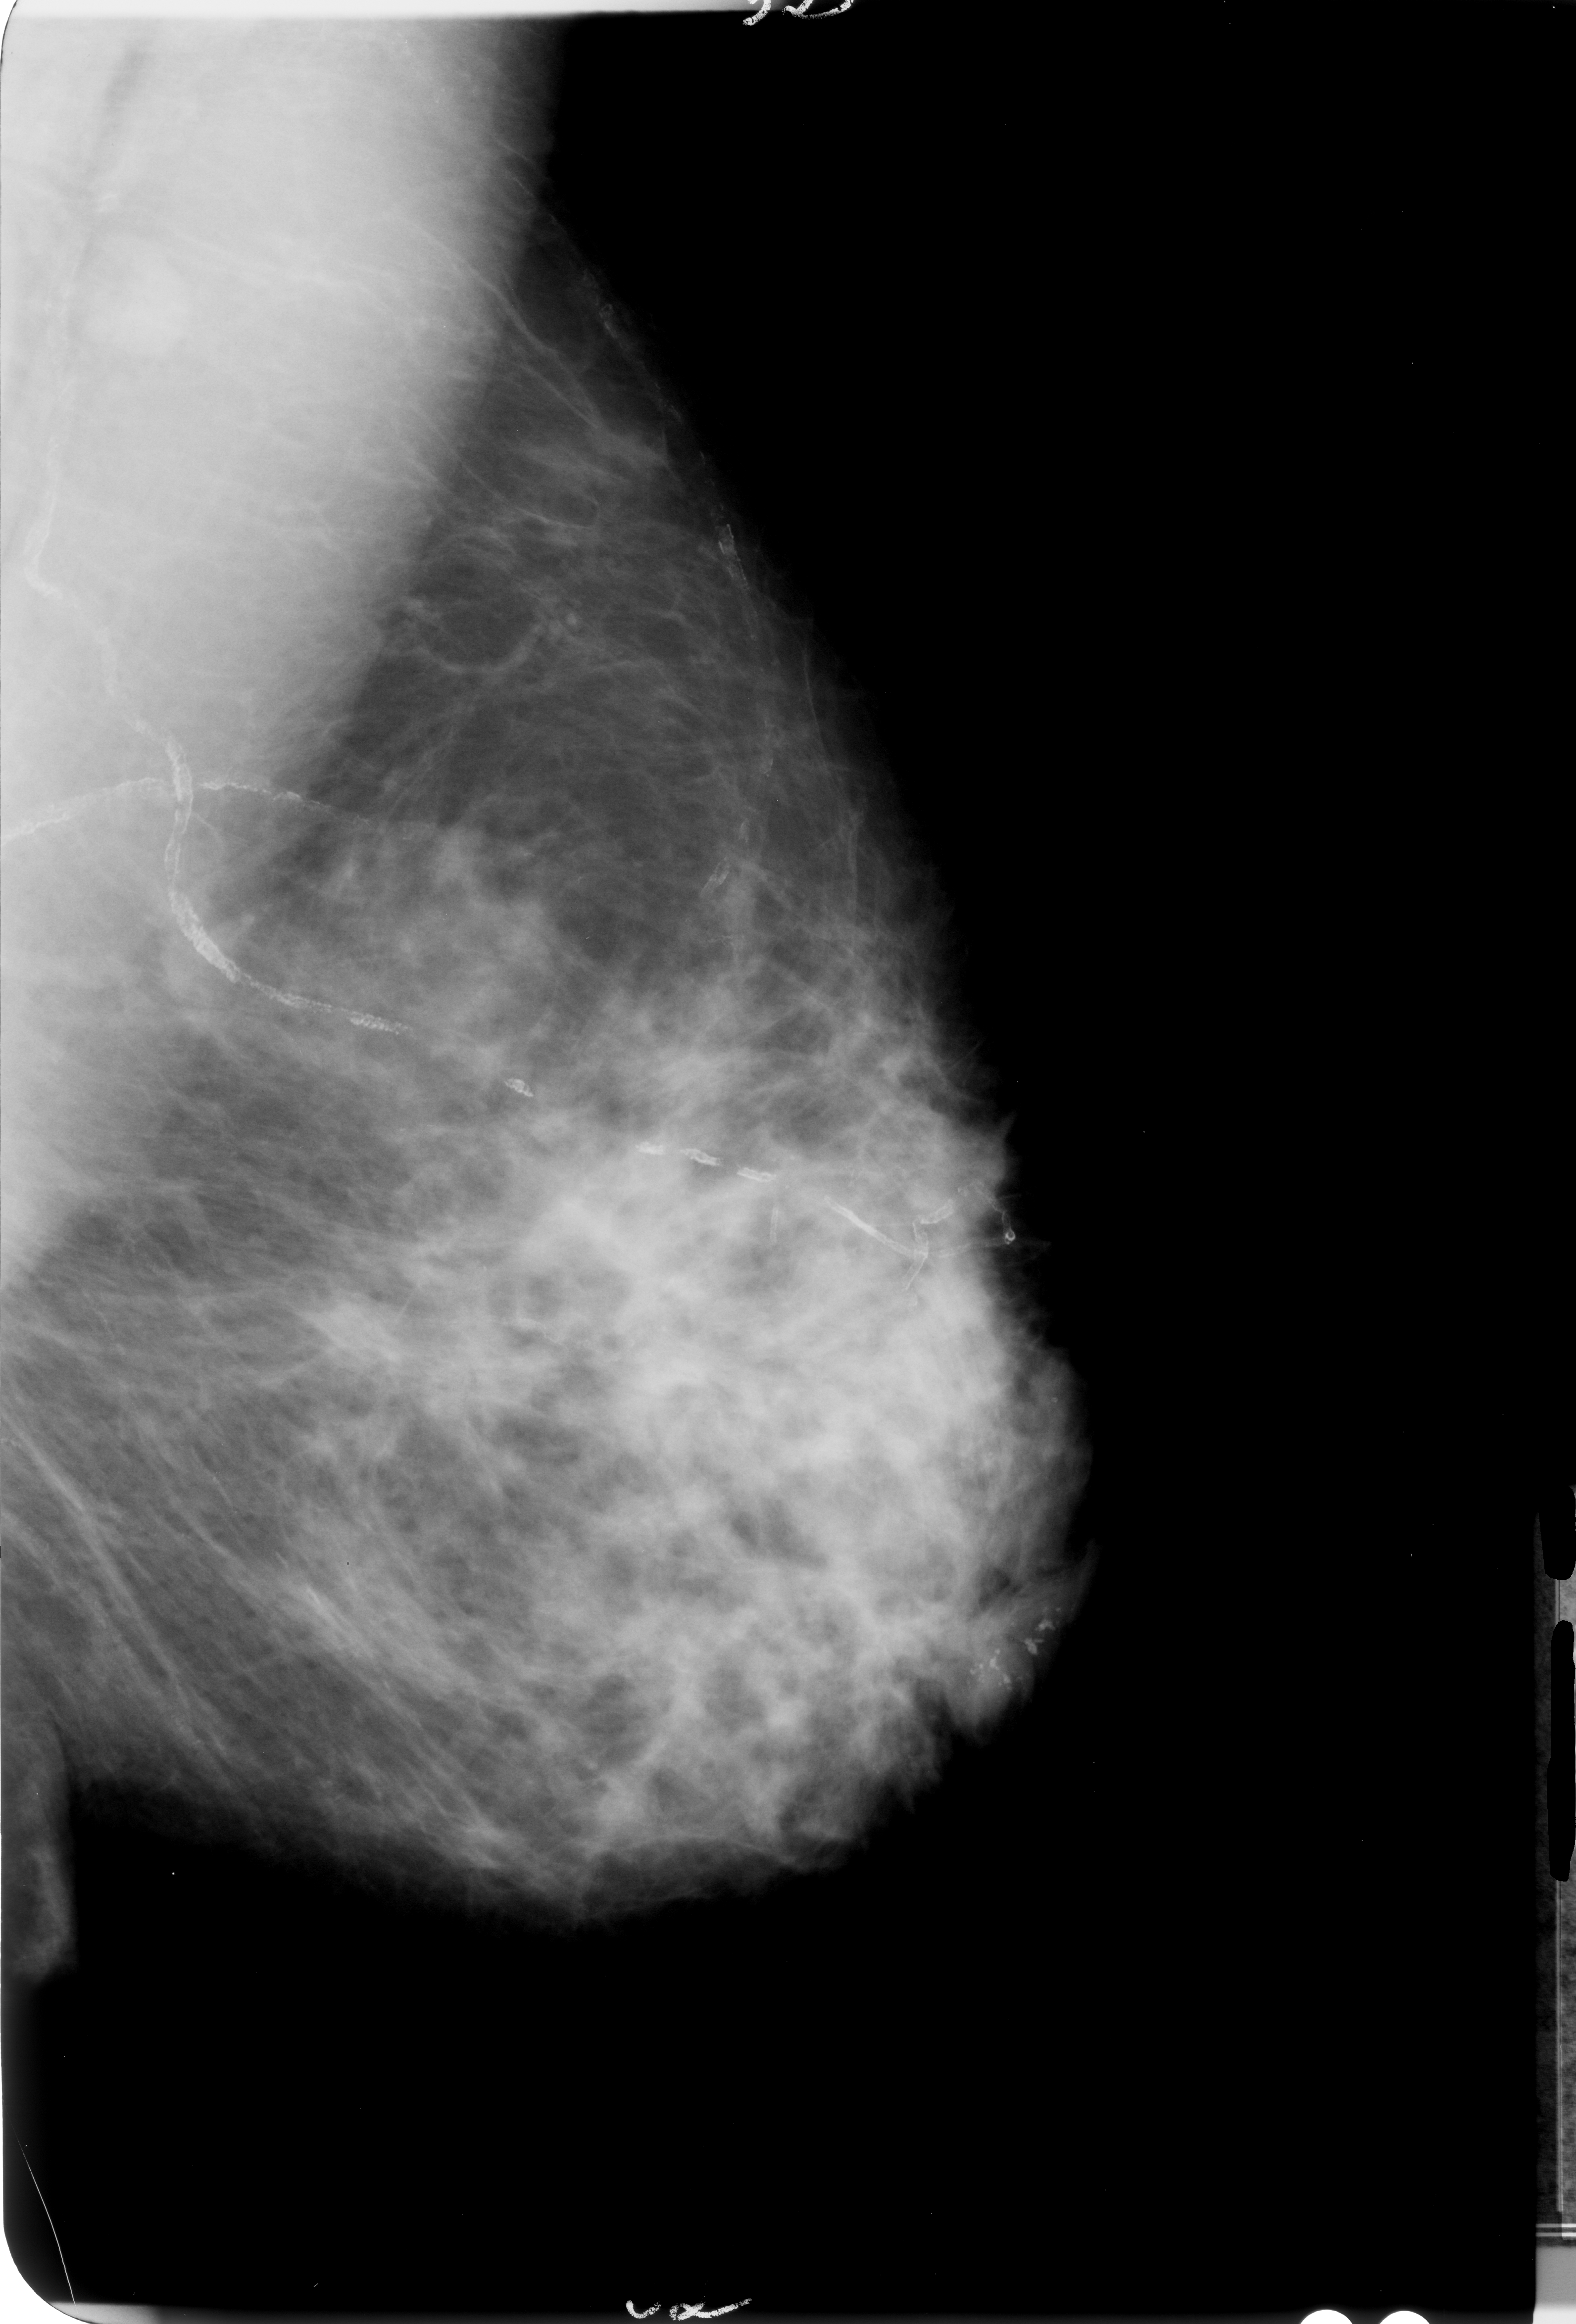
Mammogram (digitized film), left breast, mediolateral oblique (MLO) view, breast composition: scattered fibroglandular densities (BI-RADS density category 2 of 4).
Radiologist-marked abnormalities on this image: calcifications, morphology pleomorphic, distribution clustered; BI-RADS assessment category 4; subtlety rating 4 on a 1 (subtle) to 5 (obvious) scale; pathology (as recorded): malignant.